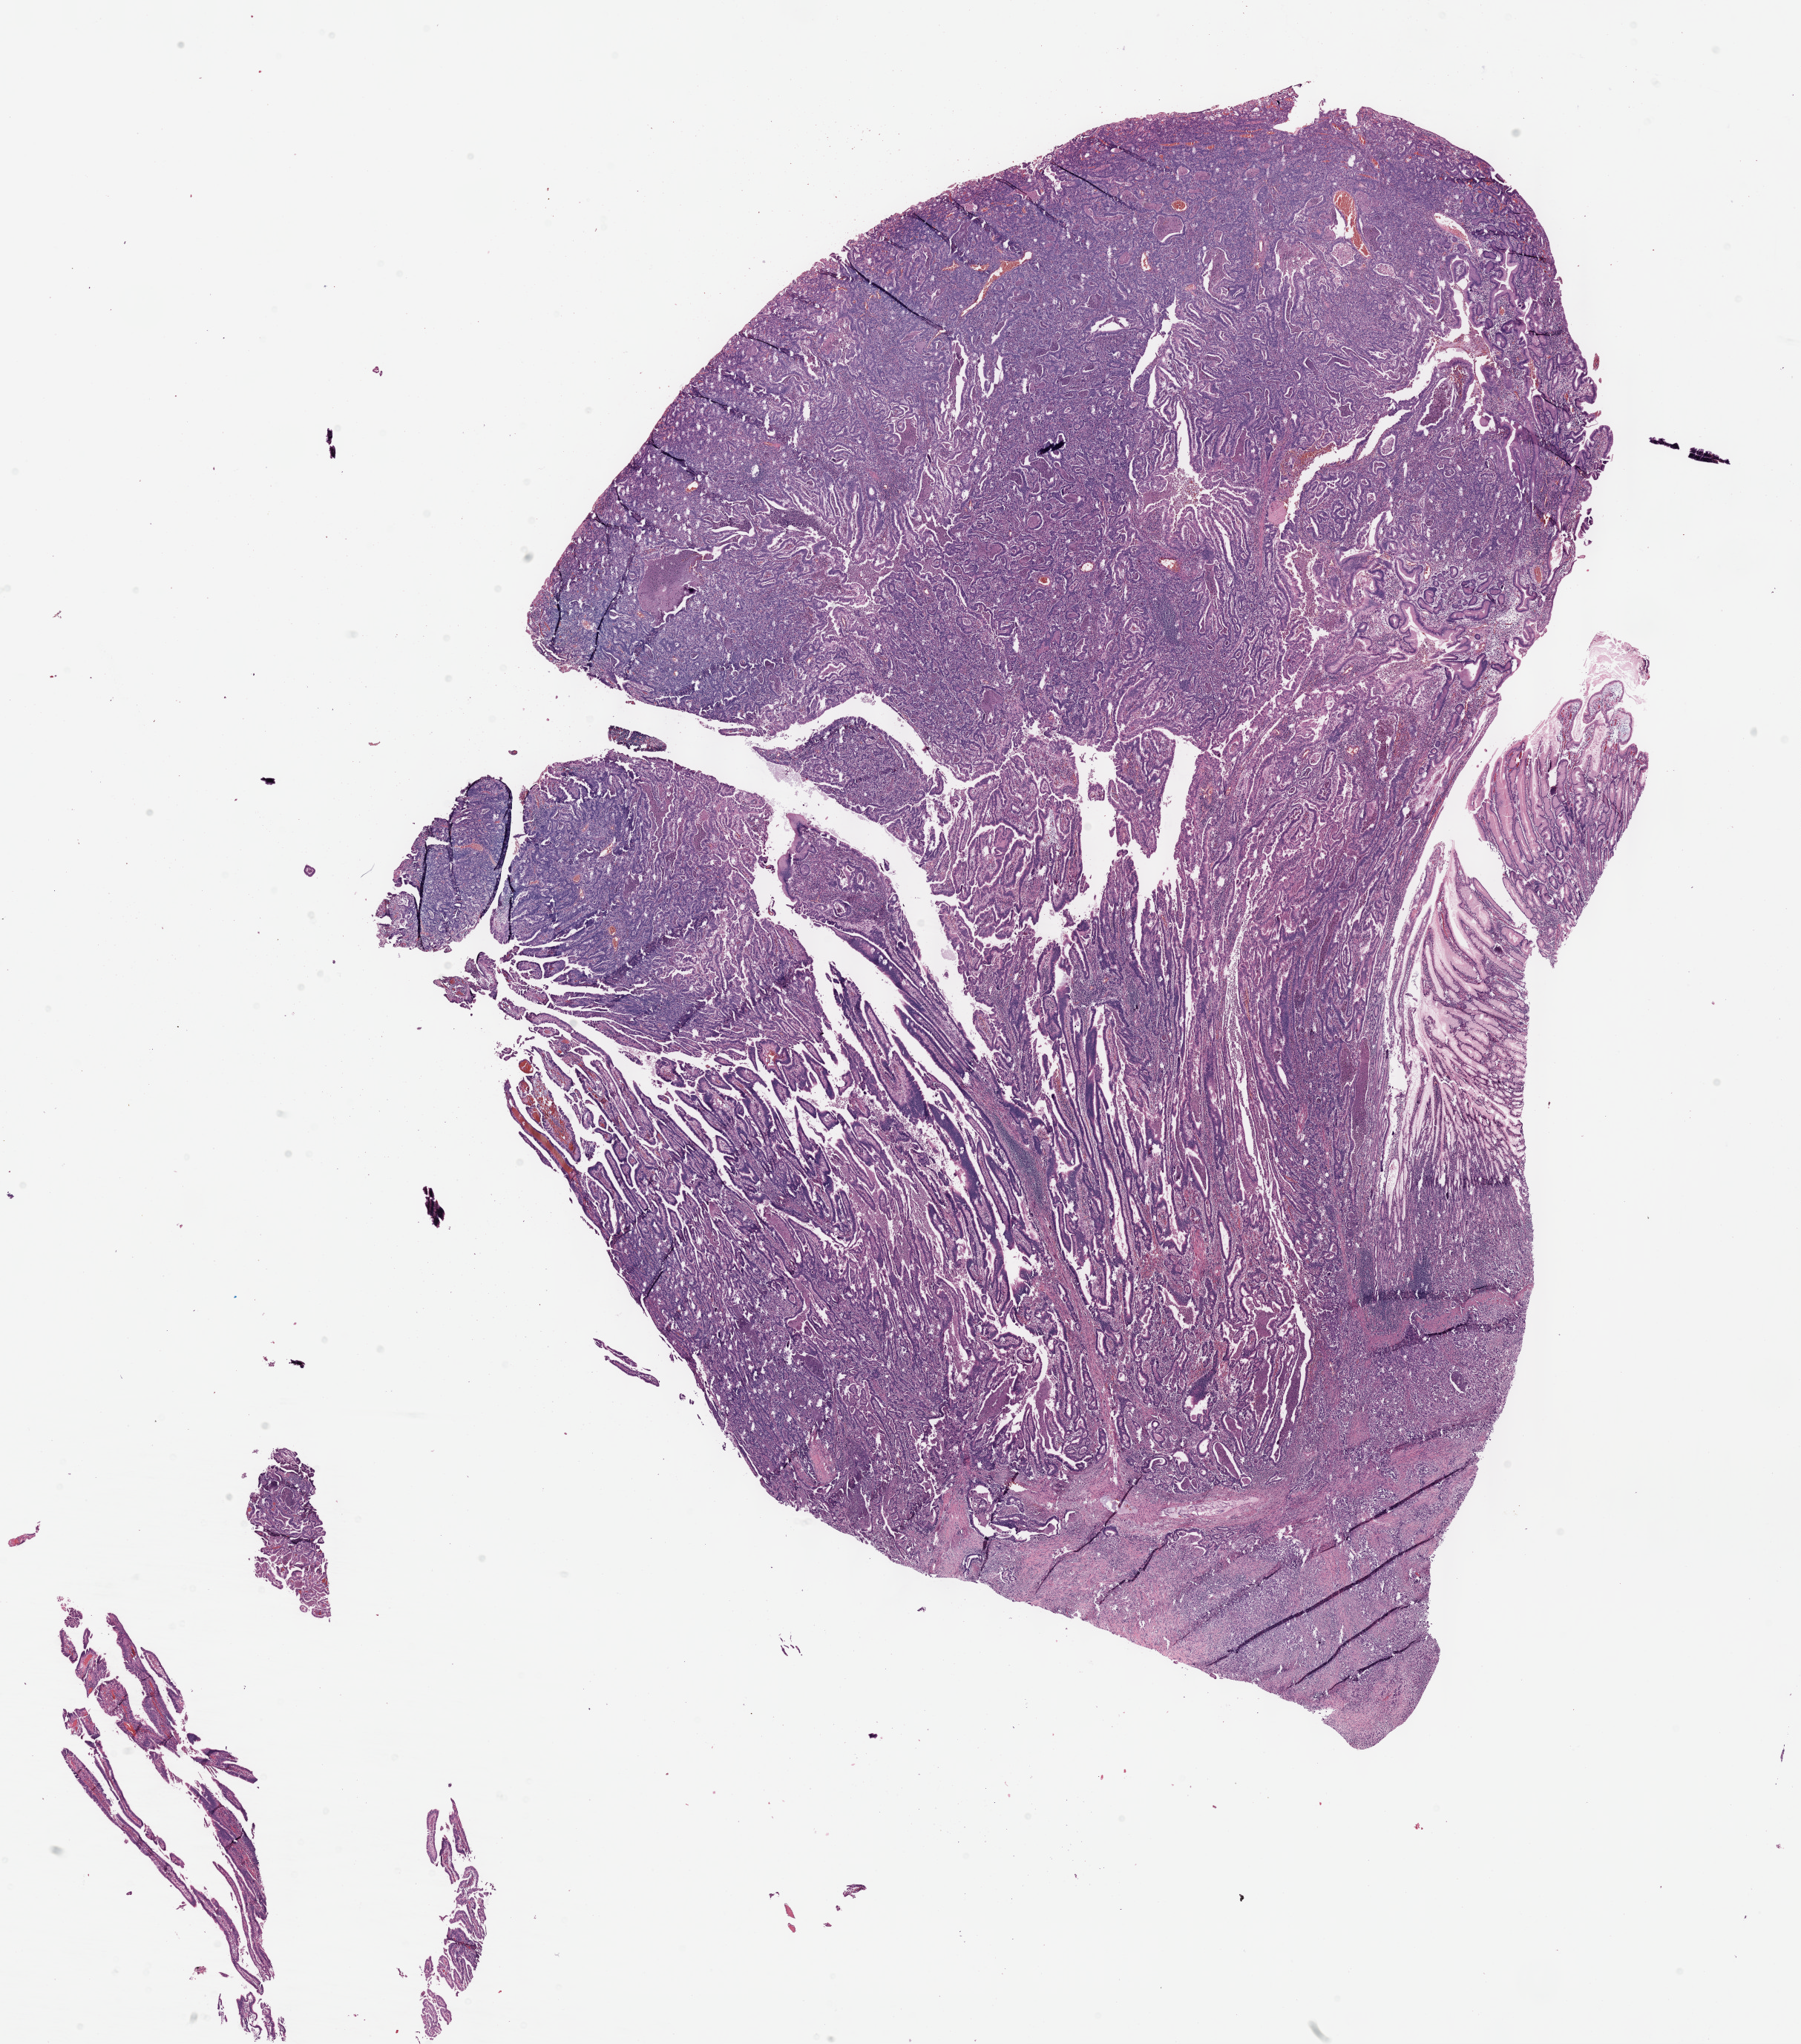
Whole-slide histology image, Hematoxylin and eosin (H&E) stained — shown as a low-resolution overview of the whole scanned area (about 19.6 x 22.3 mm, slide scanned at 40x); formalin-fixed paraffin-embedded (FFPE) diagnostic section; stomach, primary tumour sample. Female patient; age at initial diagnosis 72 years. Histologic grade: G3 (poorly differentiated).
• pathologic diagnosis: Tubular adenocarcinoma
• AJCC pathologic stage: IIIA